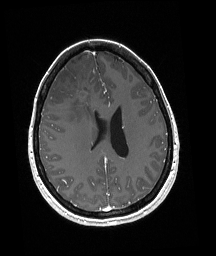
Brain MRI from a brain-tumour surgery series, one axial slice. Position 77 of 192 along the scan axis. T1-weighted post-contrast. 1 mm slice thickness. 216 × 256 image matrix, field of view 211 × 250 mm. From the clinical record (not read from this slice): histopathology: Oligodendroglioma; WHO grade: 3; IDH mutation: yes.
Structures marked on this image (expert manual segmentation):
- tumour: bounding box <59,82,86,91> (left, top, right, bottom; pixels)